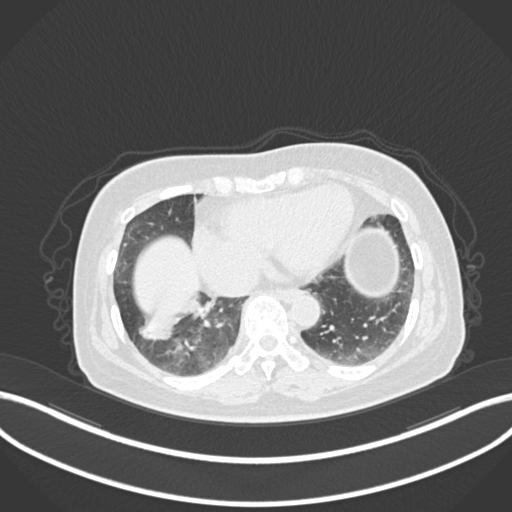
Chest CT, one axial slice; slice 34 of 222 in the series (ordered by position); reconstruction kernel B30f; lung window (W 1500 / L -600 HU); 1 mm slice thickness; 512 × 512 image matrix. Female patient, age 67 years. Case-level facts recorded for this patient, not image findings: clinical TNM (as recorded): T1c N1 M0; histopathological grade: G2-3.
Structures marked on this image (bounding box drawn by a radiologist):
- lung tumour (recorded histology: adenocarcinoma): bounding box [x1, y1, x2, y2] px = [135, 297, 202, 345]